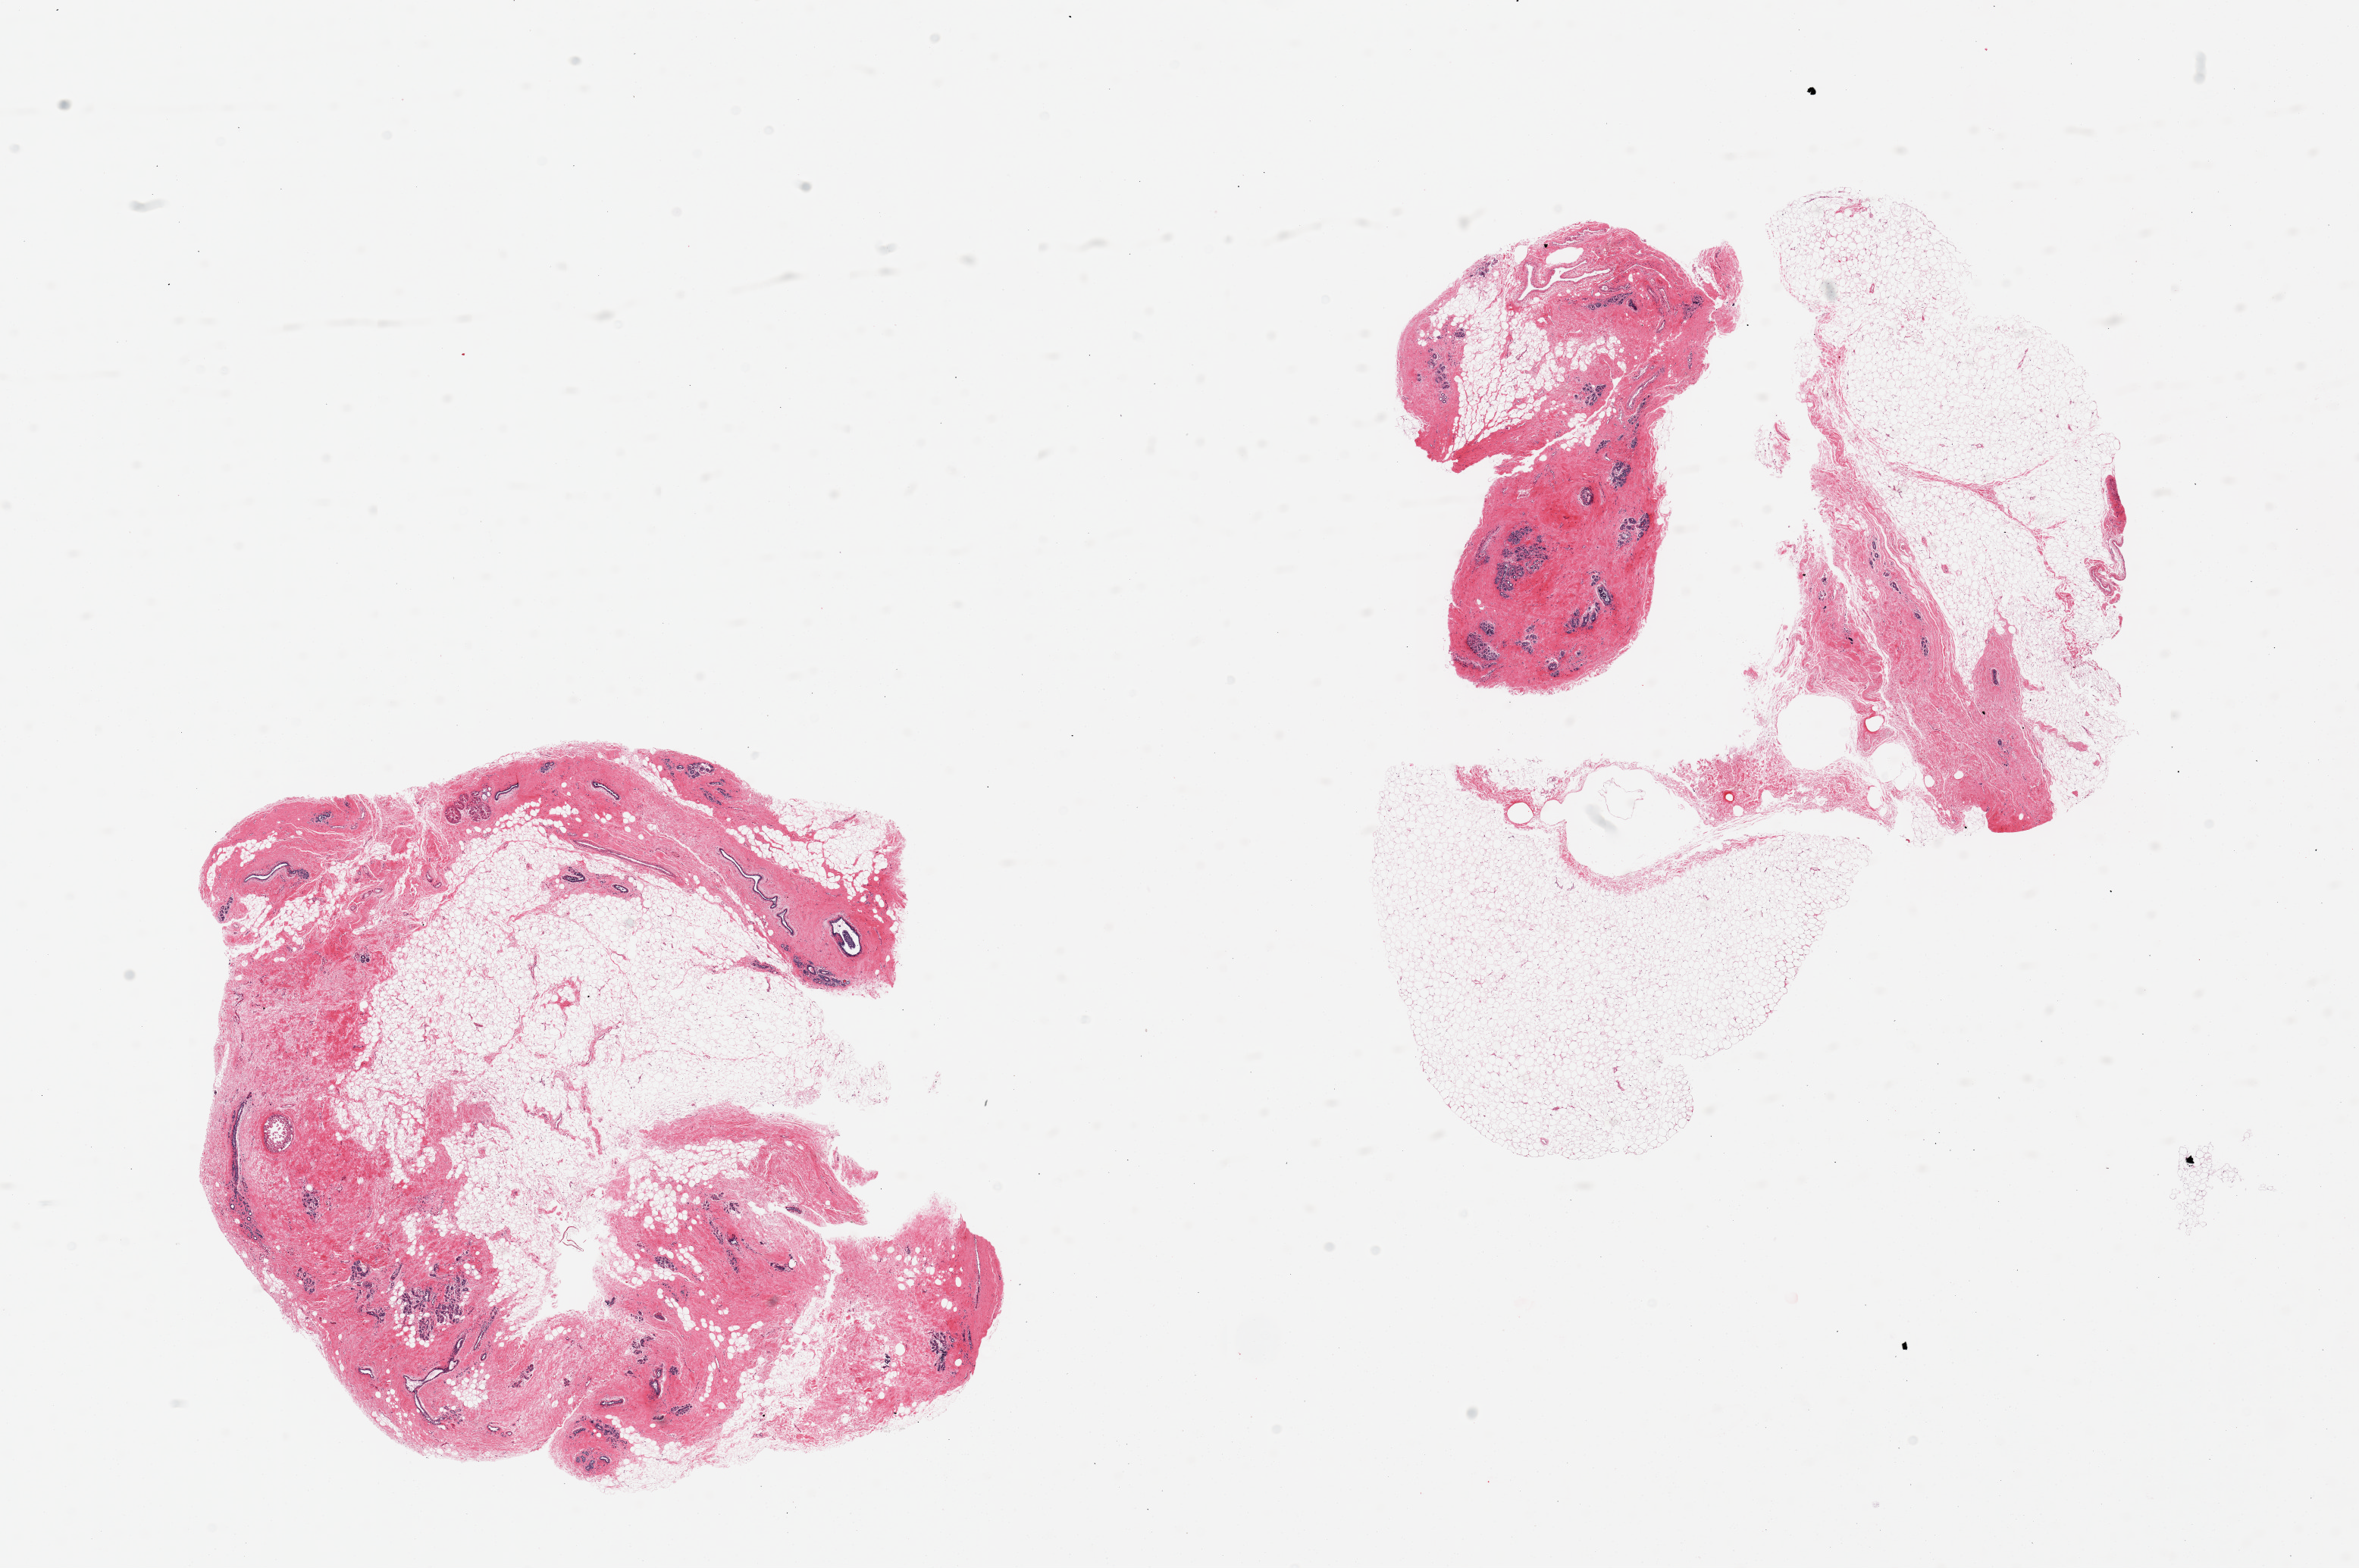
Haematoxylin and eosin whole-slide image, brightfield, whole scanned area (about 24.6 x 16.4 mm) shown as a low-resolution overview. PAXgene-fixed, paraffin-embedded tissue. Section of breast (target tissue). Donor tissue sample. Donor sex: female.
Pathologist's review note for this sample: 2 pieces, post-menopausal, involuted TLDUs present.